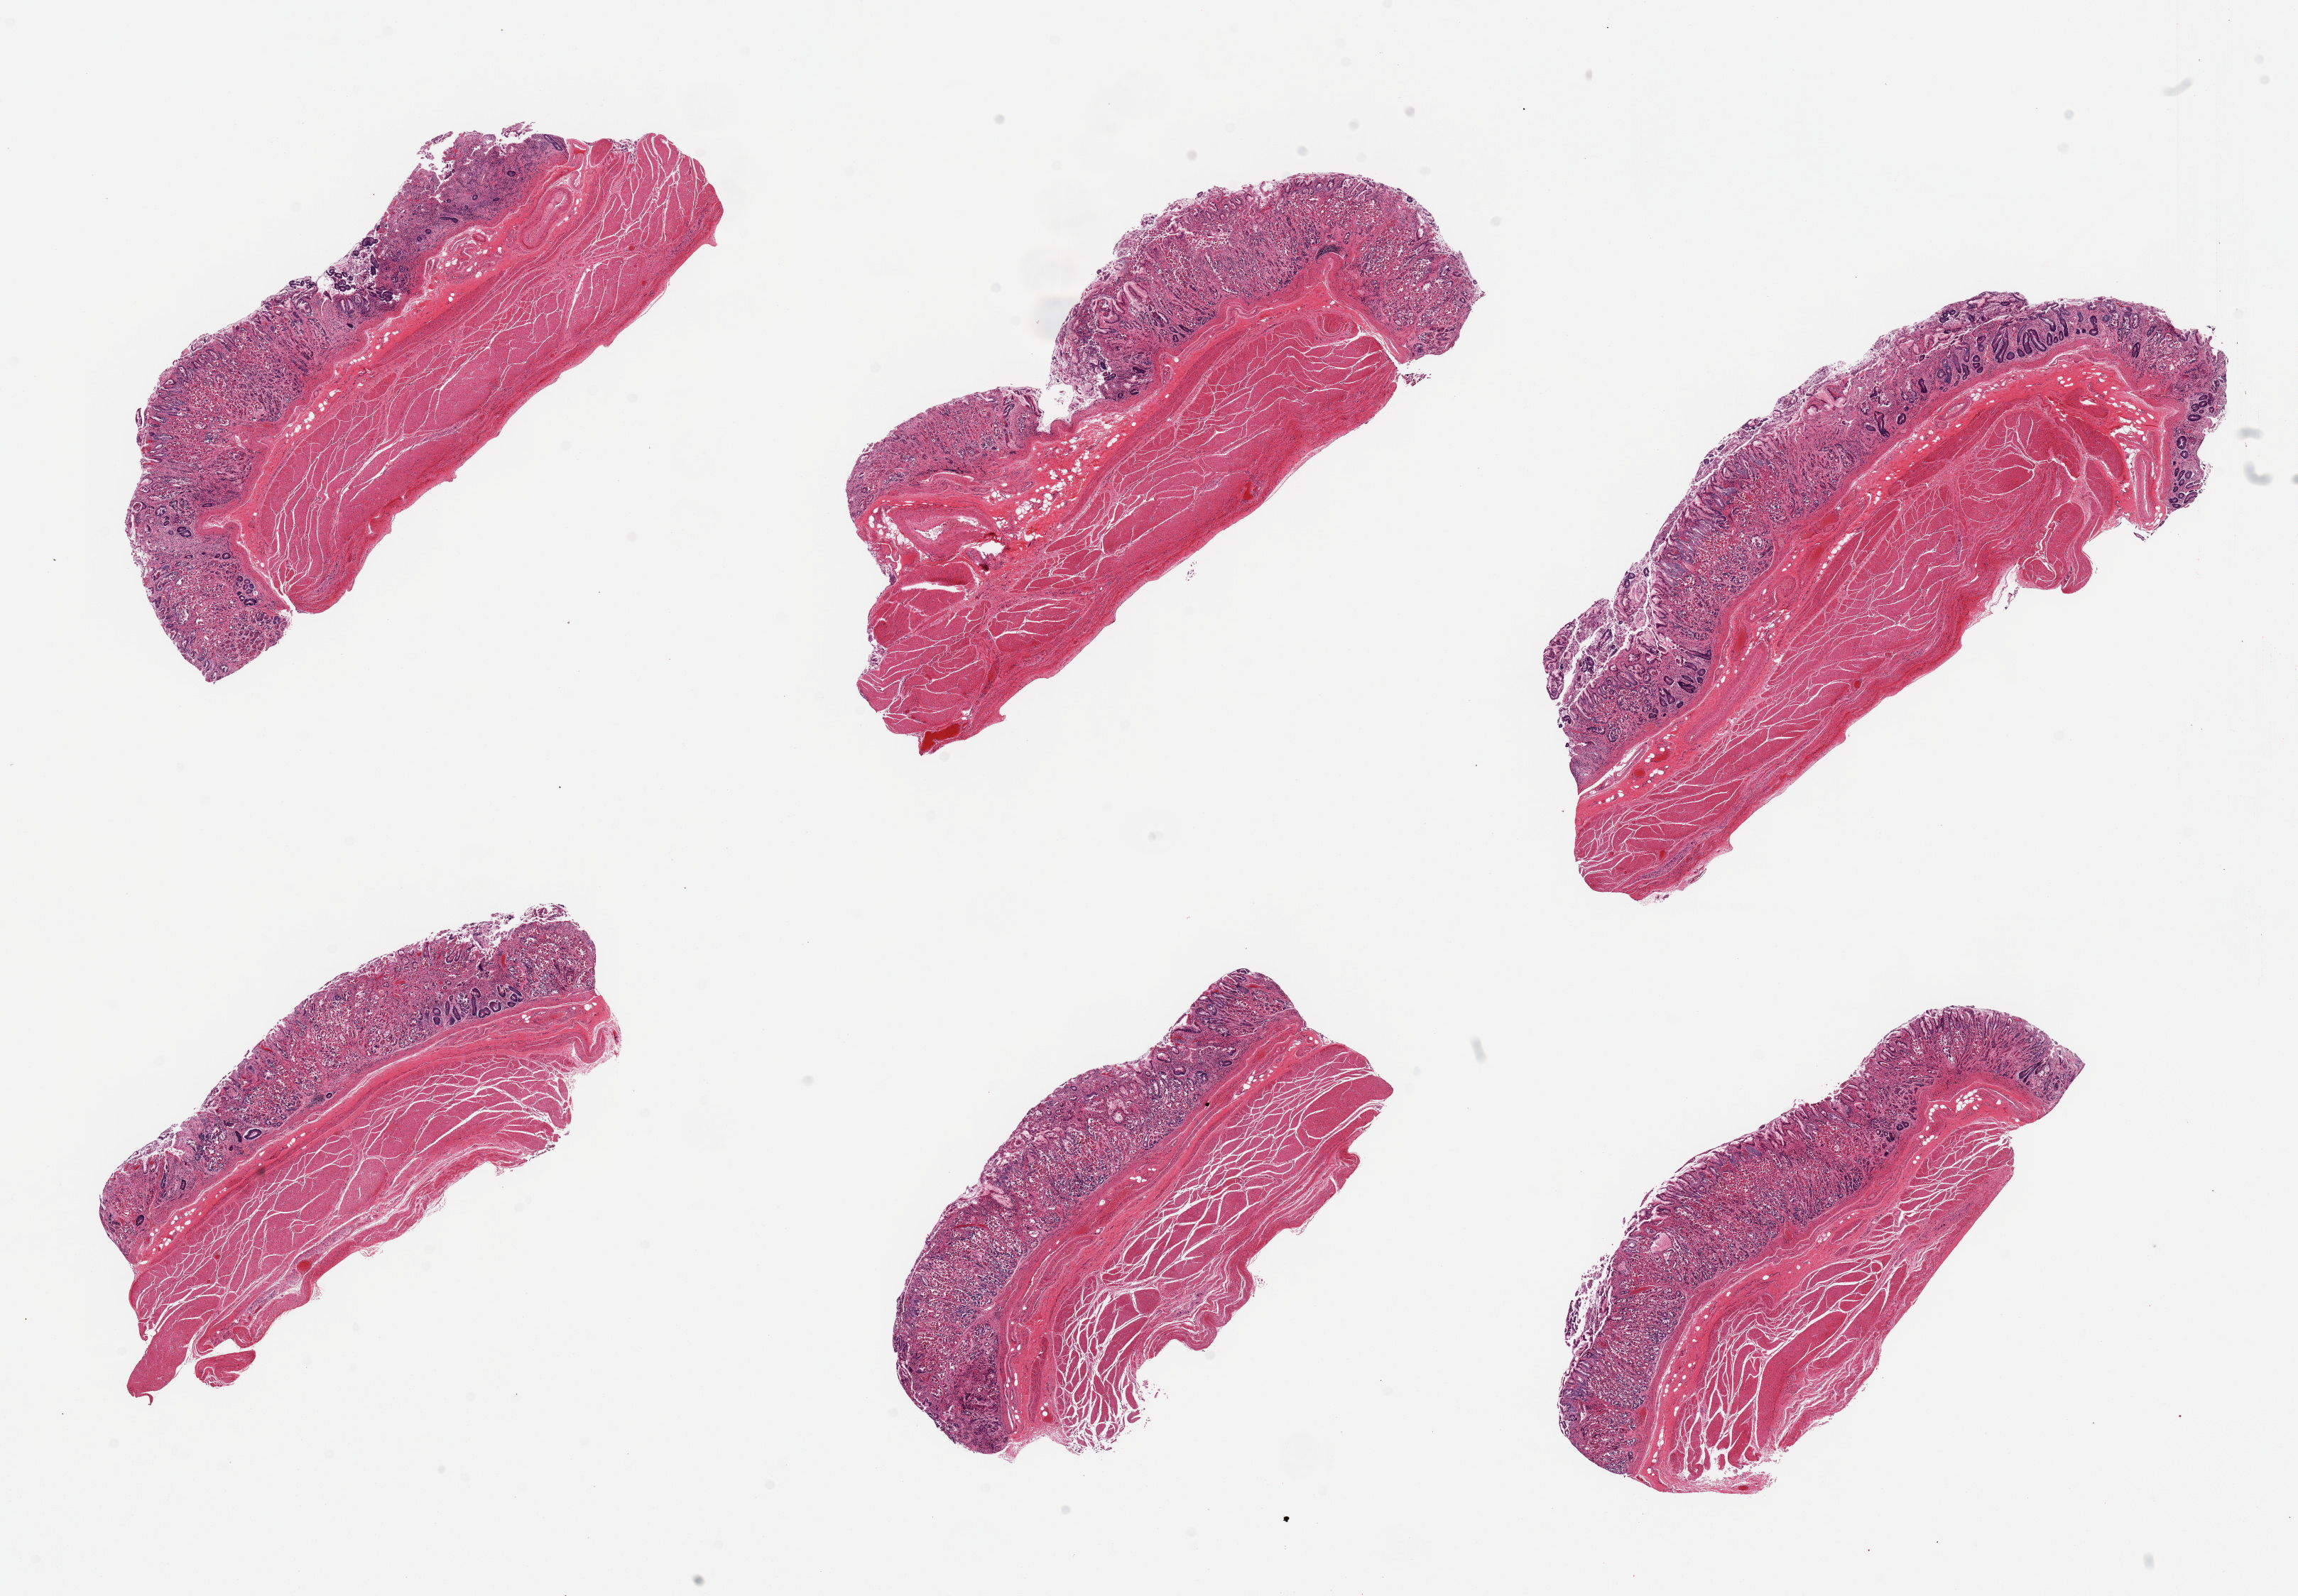
Haematoxylin and eosin whole-slide image, low-resolution overview of the scanned area, about 25.6 x 17.8 mm (acquisition: 20x scan). PAXgene-fixed, paraffin-embedded tissue. Target tissue: stomach. Tissue donor sample. Donor: male.
Pathologist's review note for this sample: 6 pieces, mucosa up to 1mm, ~40% thickness, but with advanced autolysis.